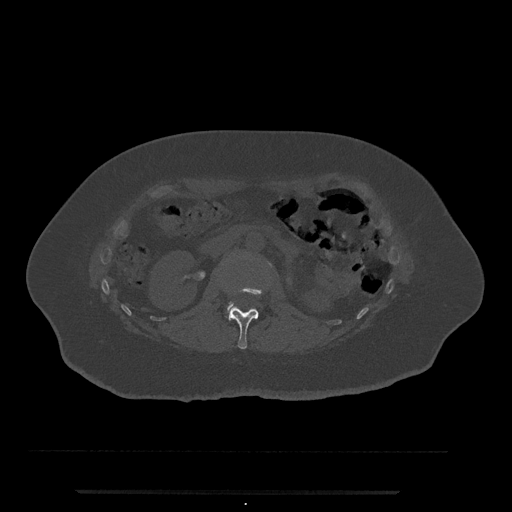
CT including the spine, one axial slice. Position 79 of 797 along the scan axis. 120 kVp. Bone window (W 1800 / L 400 HU). 512 × 512 image matrix, field of view 440 × 440 mm. Female patient, age 51 years. From the clinical record (not read from this slice): primary cancer: neuro.
Outlined on this slice (semi-automatic segmentation, software-assisted and operator-edited):
- L1 vertebra: box from (x=228, y=285) to (x=268, y=349) px
- L2 vertebra: (x=228, y=302)–(x=238, y=313)